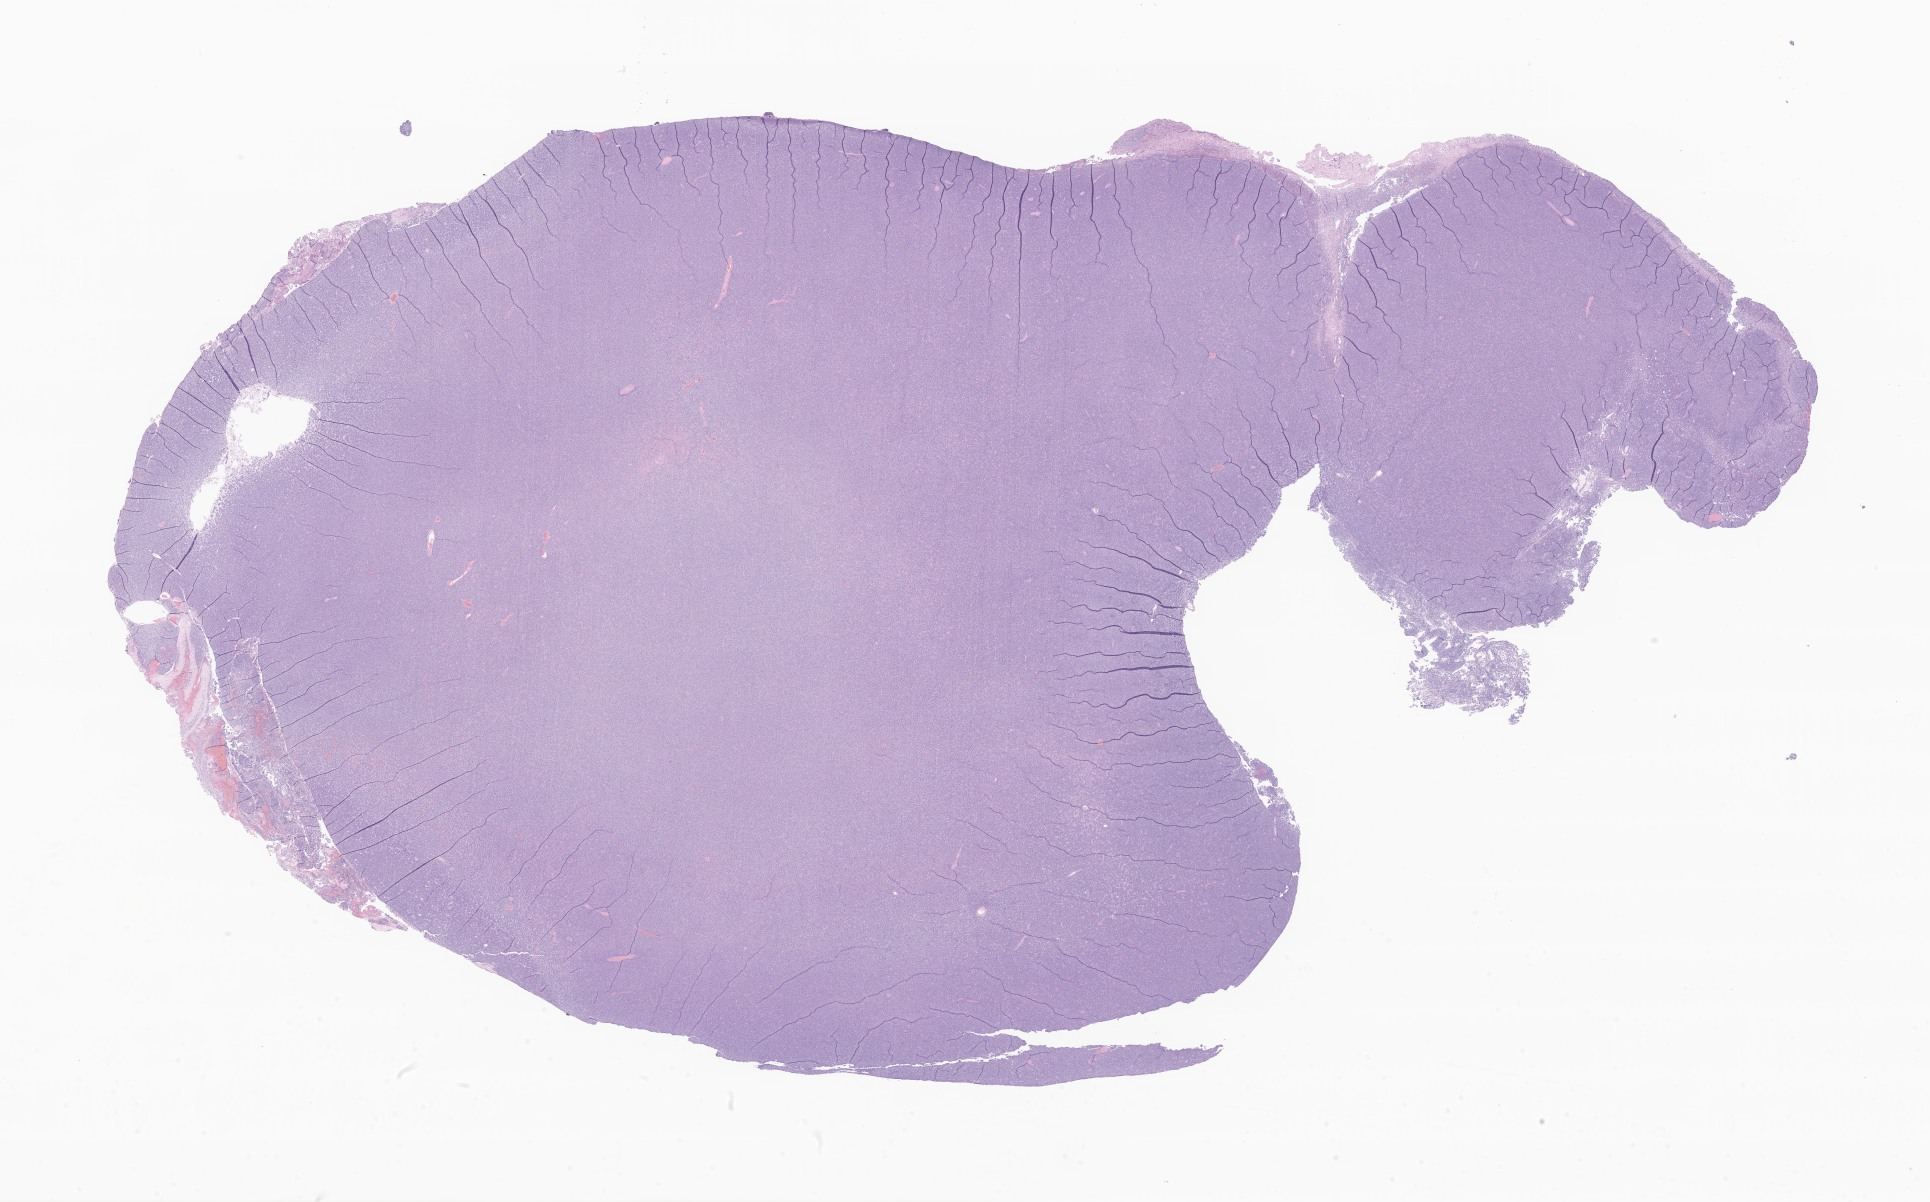
Hematoxylin and eosin (H&E) whole-slide image of tumor tissue from the brain, low-resolution overview of the scanned area, about 32.5 x 20.3 mm, formalin-fixed, paraffin-embedded (FFPE) tissue. Patient female; age 204 months (17 years).
Diagnosis: Medulloblastoma, NOS.